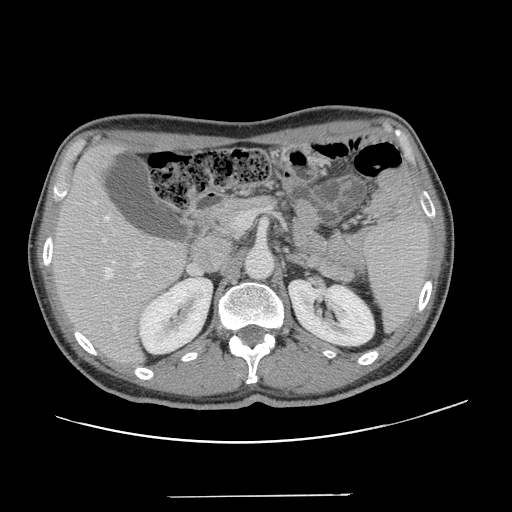
Contrast-enhanced abdominal CT, one axial slice. Slice 77 of 131 in the series (ordered by position). 120 kVp. Intravenous contrast given. Soft-tissue window (W 400 / L 40 HU). 2.5 mm slice thickness. 512 × 512 image matrix, field of view 403 × 403 mm. Male patient, age 60 years. Case-level facts recorded for this patient, not image findings: diagnosis: colorectal cancer liver metastases, imaged before liver resection; multiple liver metastases: no; largest metastasis: 2.5 cm; chemotherapy before resection: no.
Annotated regions visible in this slice (outlined manually by an expert reader):
- hepatic veins: bounding box (x1, y1, x2, y2) in pixels: (94, 202, 140, 279)
- liver: (53, 146, 185, 364)
- planned liver remnant (the part of the liver to remain after resection): (53, 147, 185, 361)